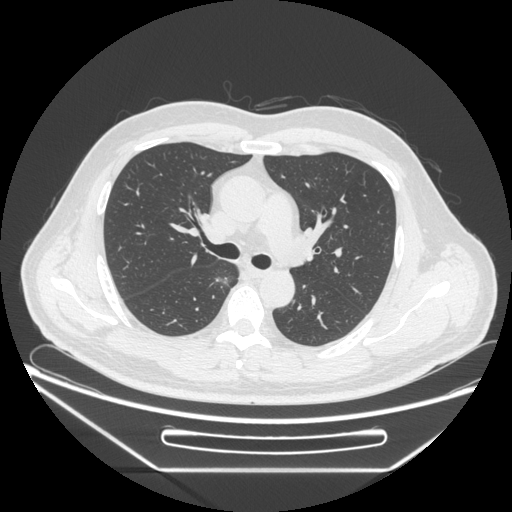
Chest CT, one axial slice; slice 161 of 271 in the series (ordered by position); lung window (W 1500 / L -600 HU); 1.25 mm slice thickness; 512 × 512 image matrix. Patient: male, 49 years. From the clinical record (not read from this slice): clinical TNM (as recorded): T1b N0 M0; histopathological grade: G2.
Annotated regions visible in this slice (rectangle marked by the reading radiologist):
- lung tumour (recorded histology: adenocarcinoma): box from (x=212, y=272) to (x=234, y=295) px